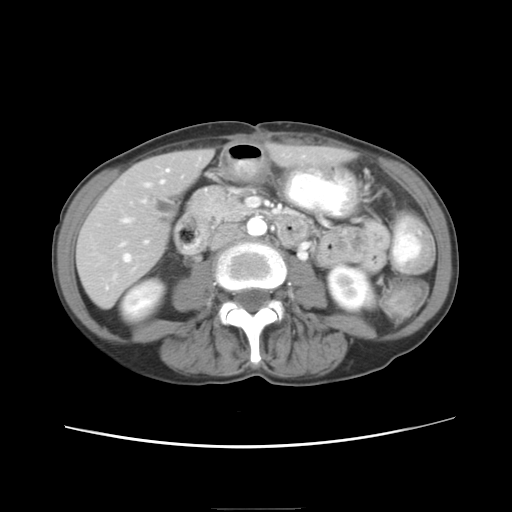
Contrast-enhanced abdominal CT, one axial slice; position 5 of 26 along the scan axis; intravenous contrast given; soft-tissue window (W 400 / L 40 HU); 512 × 512 image matrix, field of view 340 × 340 mm. Female patient, age 65 years. Case-level facts recorded for this patient, not image findings: diagnosis: colorectal cancer liver metastases, imaged before liver resection; multiple liver metastases: no; disease in both lobes: yes.
Structures marked on this image (manually delineated by an expert):
- hepatic veins: bounding box (x1, y1, x2, y2) in pixels: (122, 169, 169, 261)
- liver: (77, 149, 336, 305)
- planned liver remnant (the part of the liver to remain after resection): (78, 149, 334, 305)
- portal vein (with intrahepatic branches): (121, 200, 145, 246)